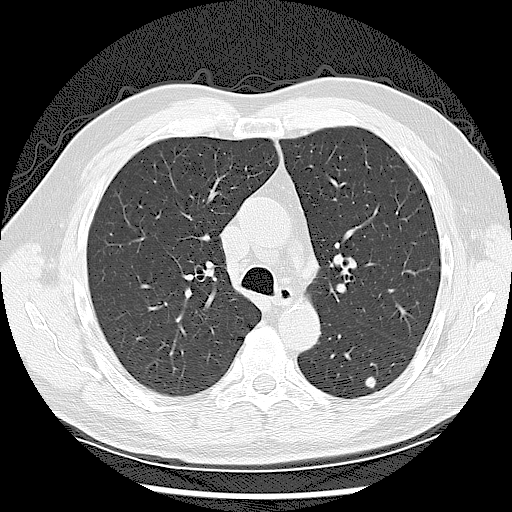
Axial slice from a low-dose chest CT screening exam. Baseline annual screen. Lung window (W 1500 / L -600 HU). 2.5 mm slice thickness. Male participant, aged 65 years at enrolment. Former smoker at enrolment.
- Lesion marked by an expert reader, box from (x=353, y=367) to (x=396, y=403) px.
- Screening reader's record for this exam (one nodule recorded; not confirmed to be the boxed lesion): non-calcified nodule or mass ≥4 mm, left lower lobe, 7 × 7 mm, smooth margins, soft tissue attenuation.
- Official screen result: positive, change unspecified: nodule(s) >= 4 mm or enlarging nodule(s), mass(es), or other non-specific abnormalities suspicious for lung cancer.
- Lung cancer was diagnosed 375 days after this screen: adenocarcinoma, NOS, left lower lobe, well differentiated (G1), stage IB (AJCC 6th edition), 10 mm at pathology.